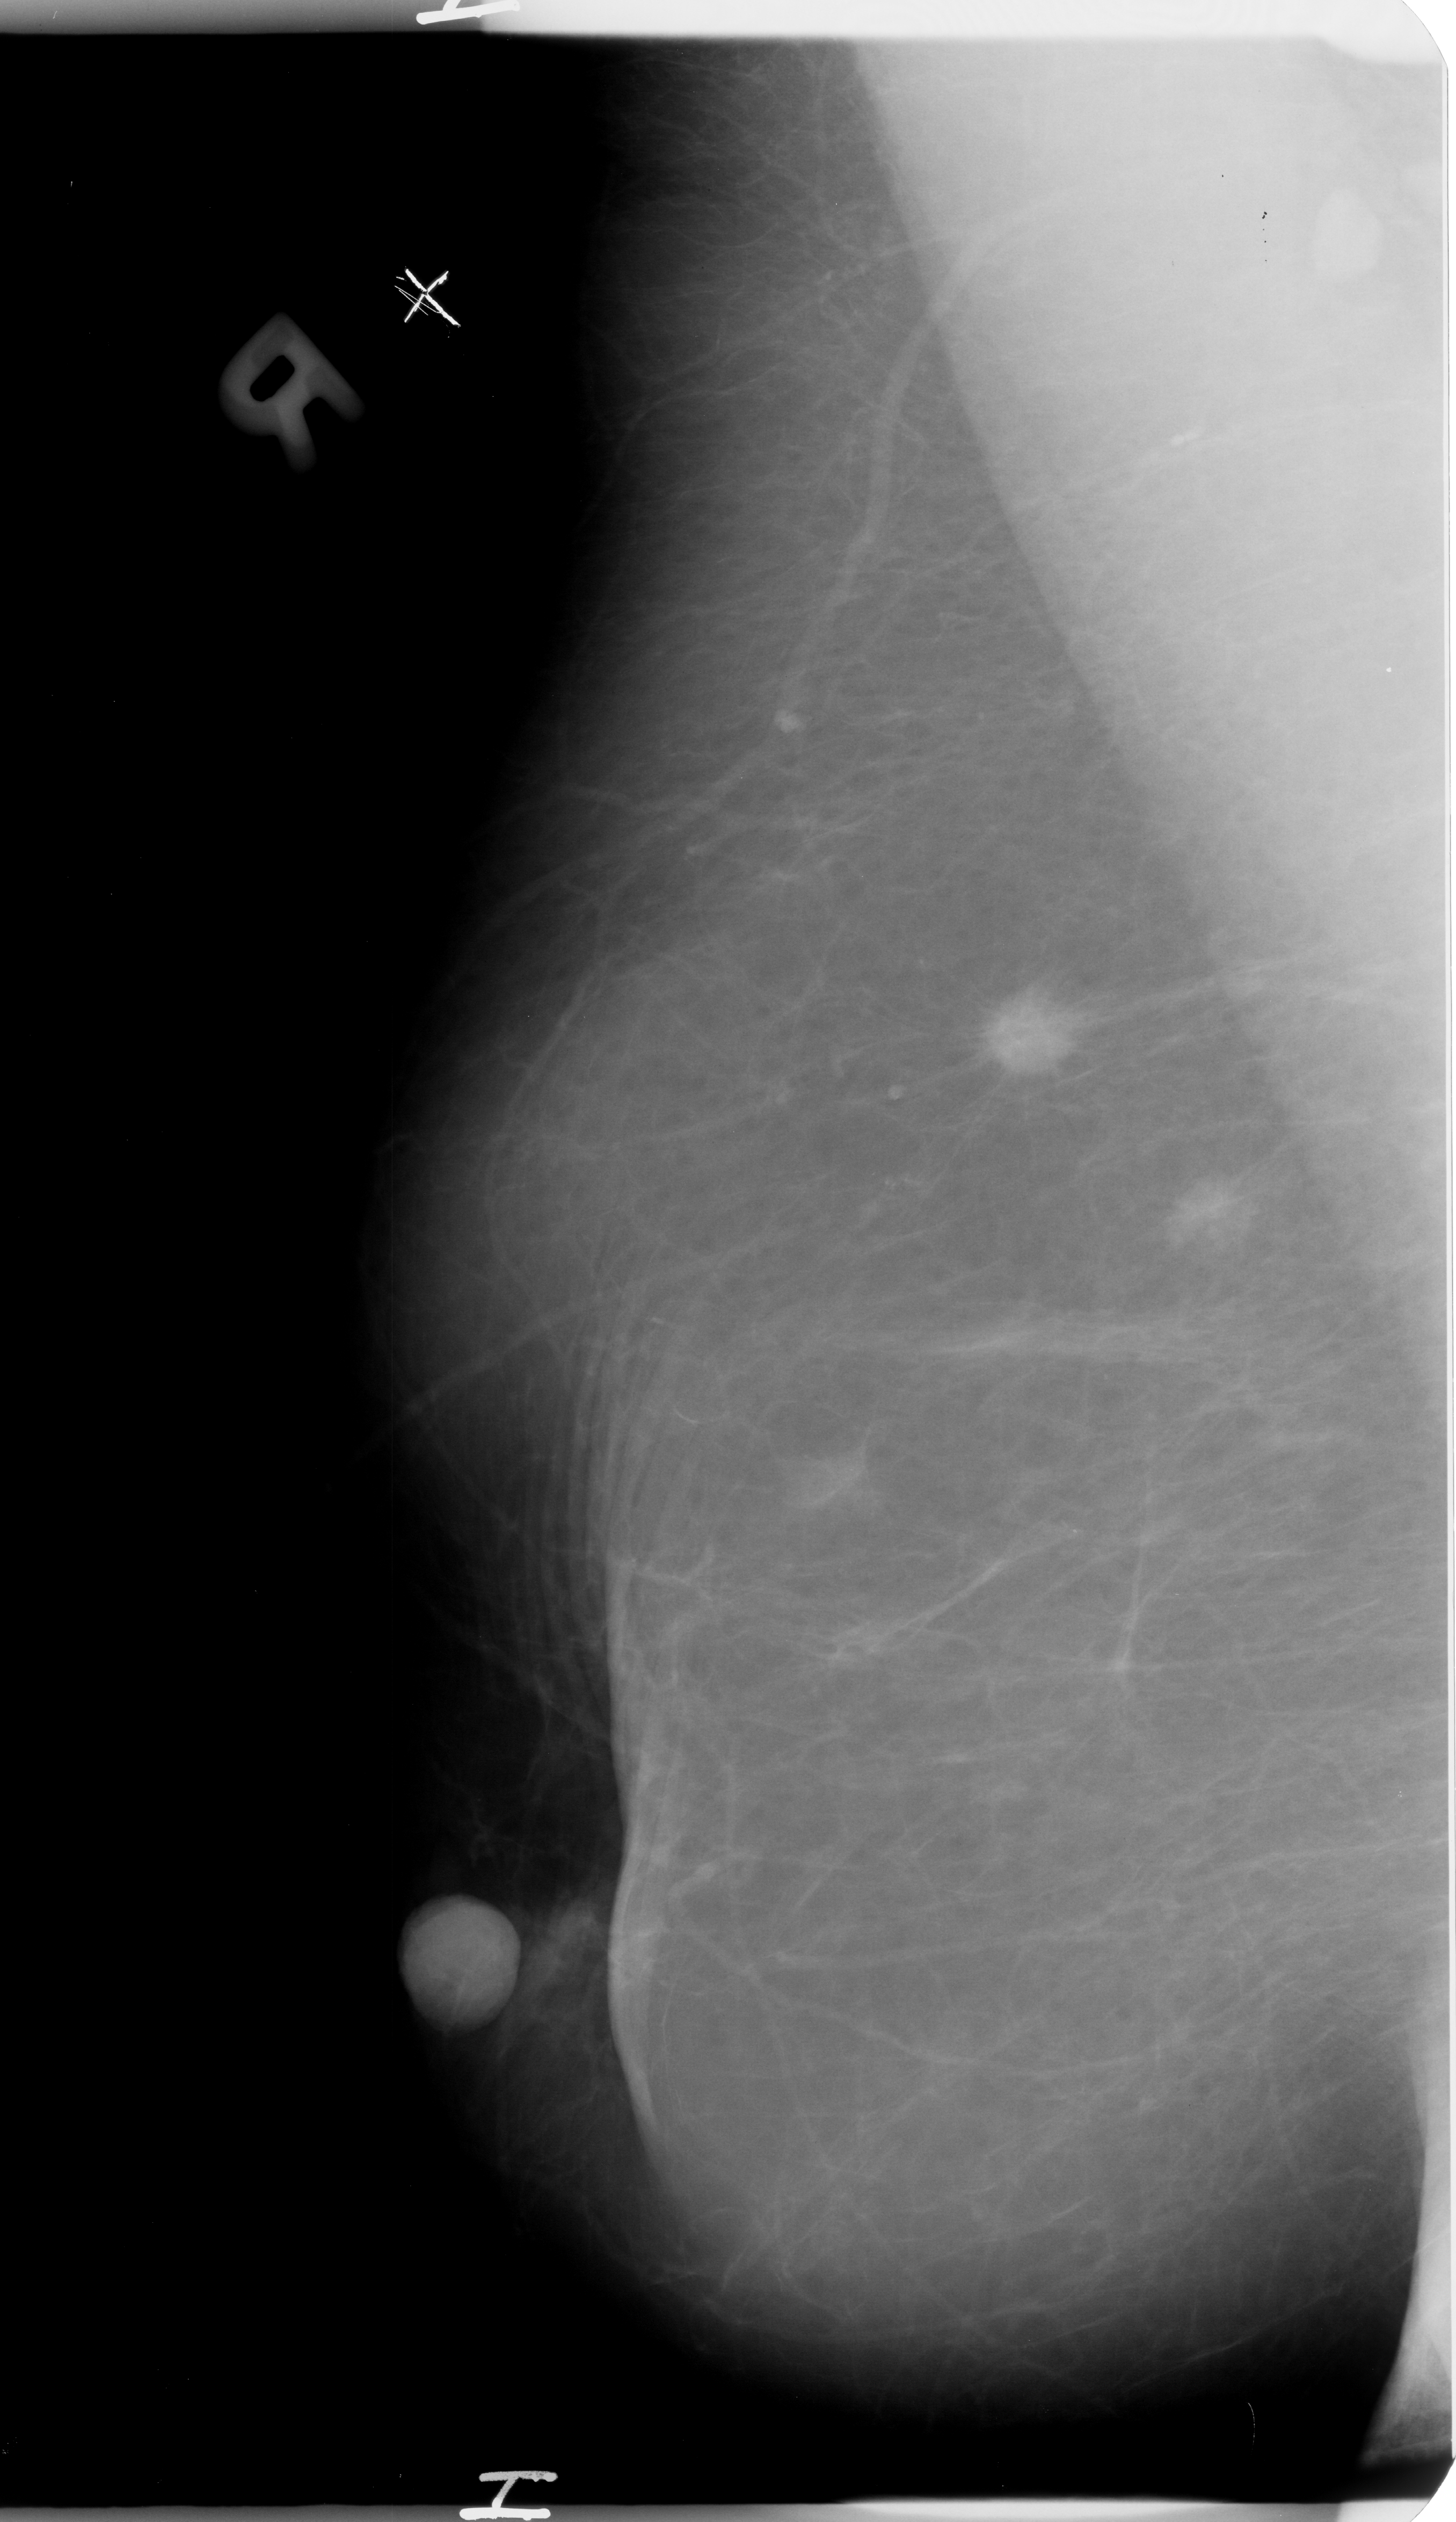
Mammogram (digitized film), right breast, mediolateral oblique (MLO) view, breast composition: almost entirely fatty (BI-RADS density category 1 of 4).
Marked abnormality: mass, shape irregular, margins spiculated; BI-RADS assessment category 4; pathology result (as recorded, not read from the image): malignant.